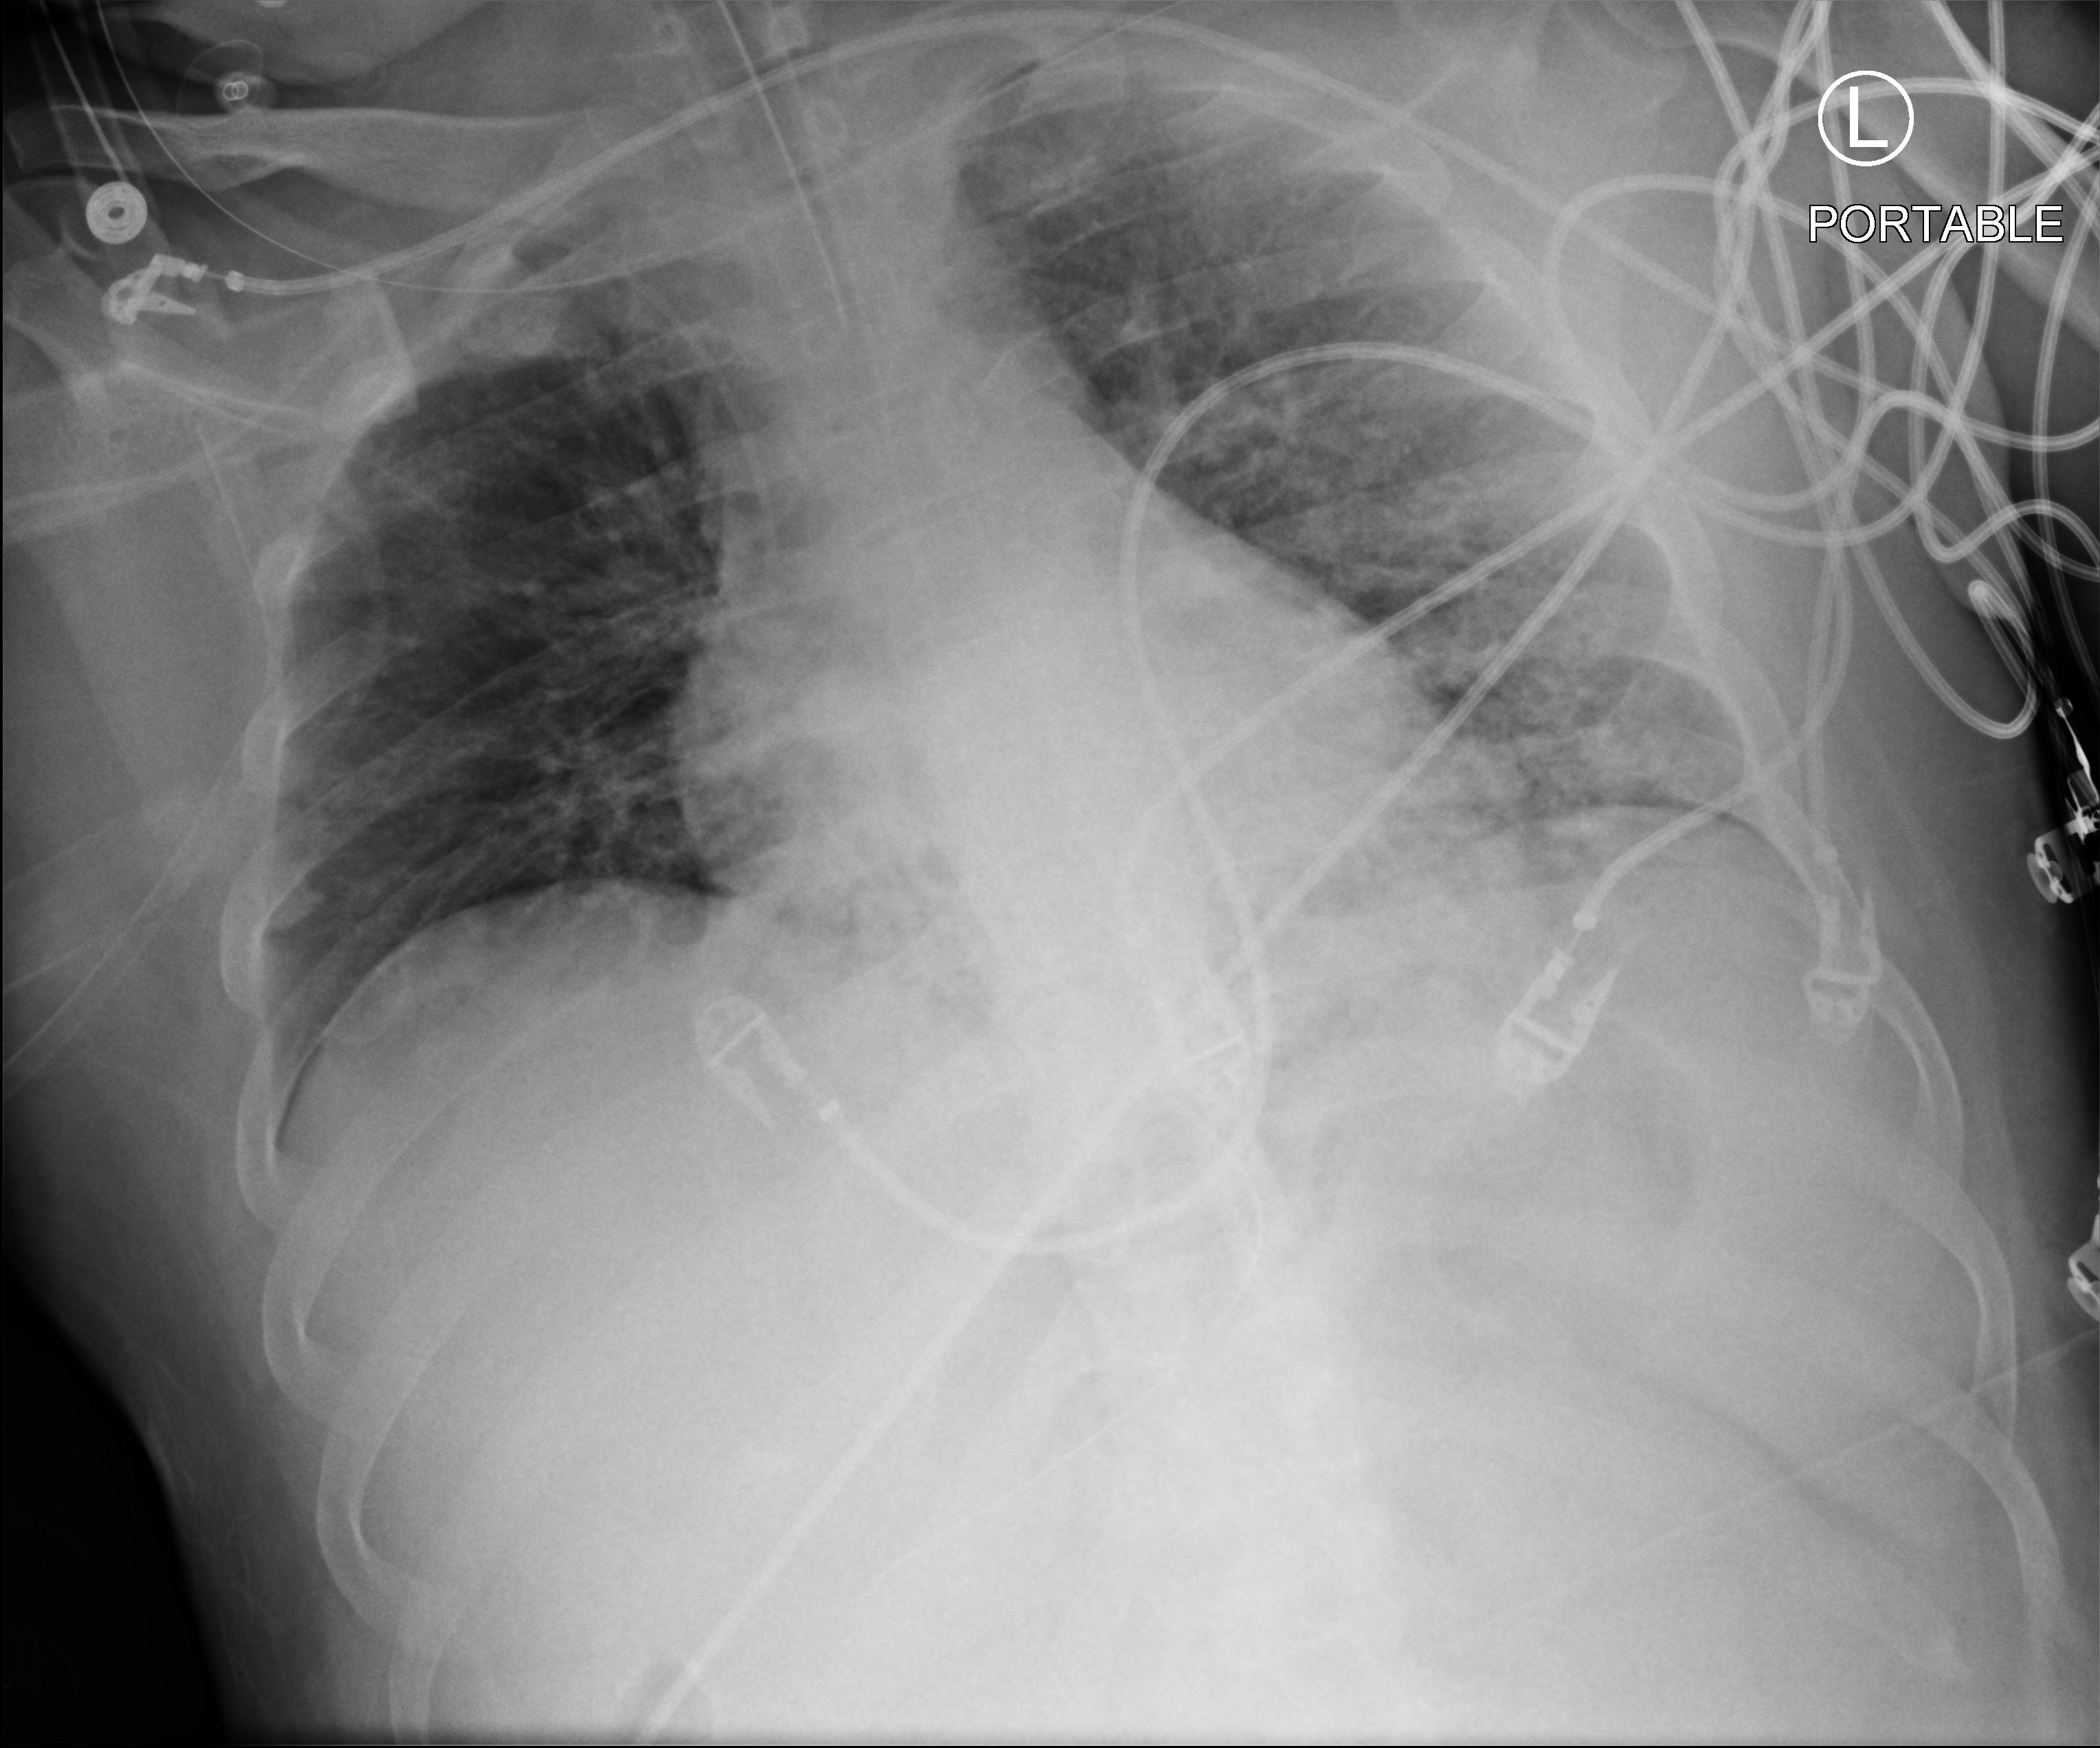
Bedside chest radiograph (computed radiography); anteroposterior (AP) projection. Male patient hospitalised with COVID-19, age 18–59 years.
From the hospital-stay record, not from the radiograph (when in the stay this image was taken is not recorded):
- hypertension (admission record): no
- smoking status (admission record): former
- mechanically ventilated during this hospital stay: yes